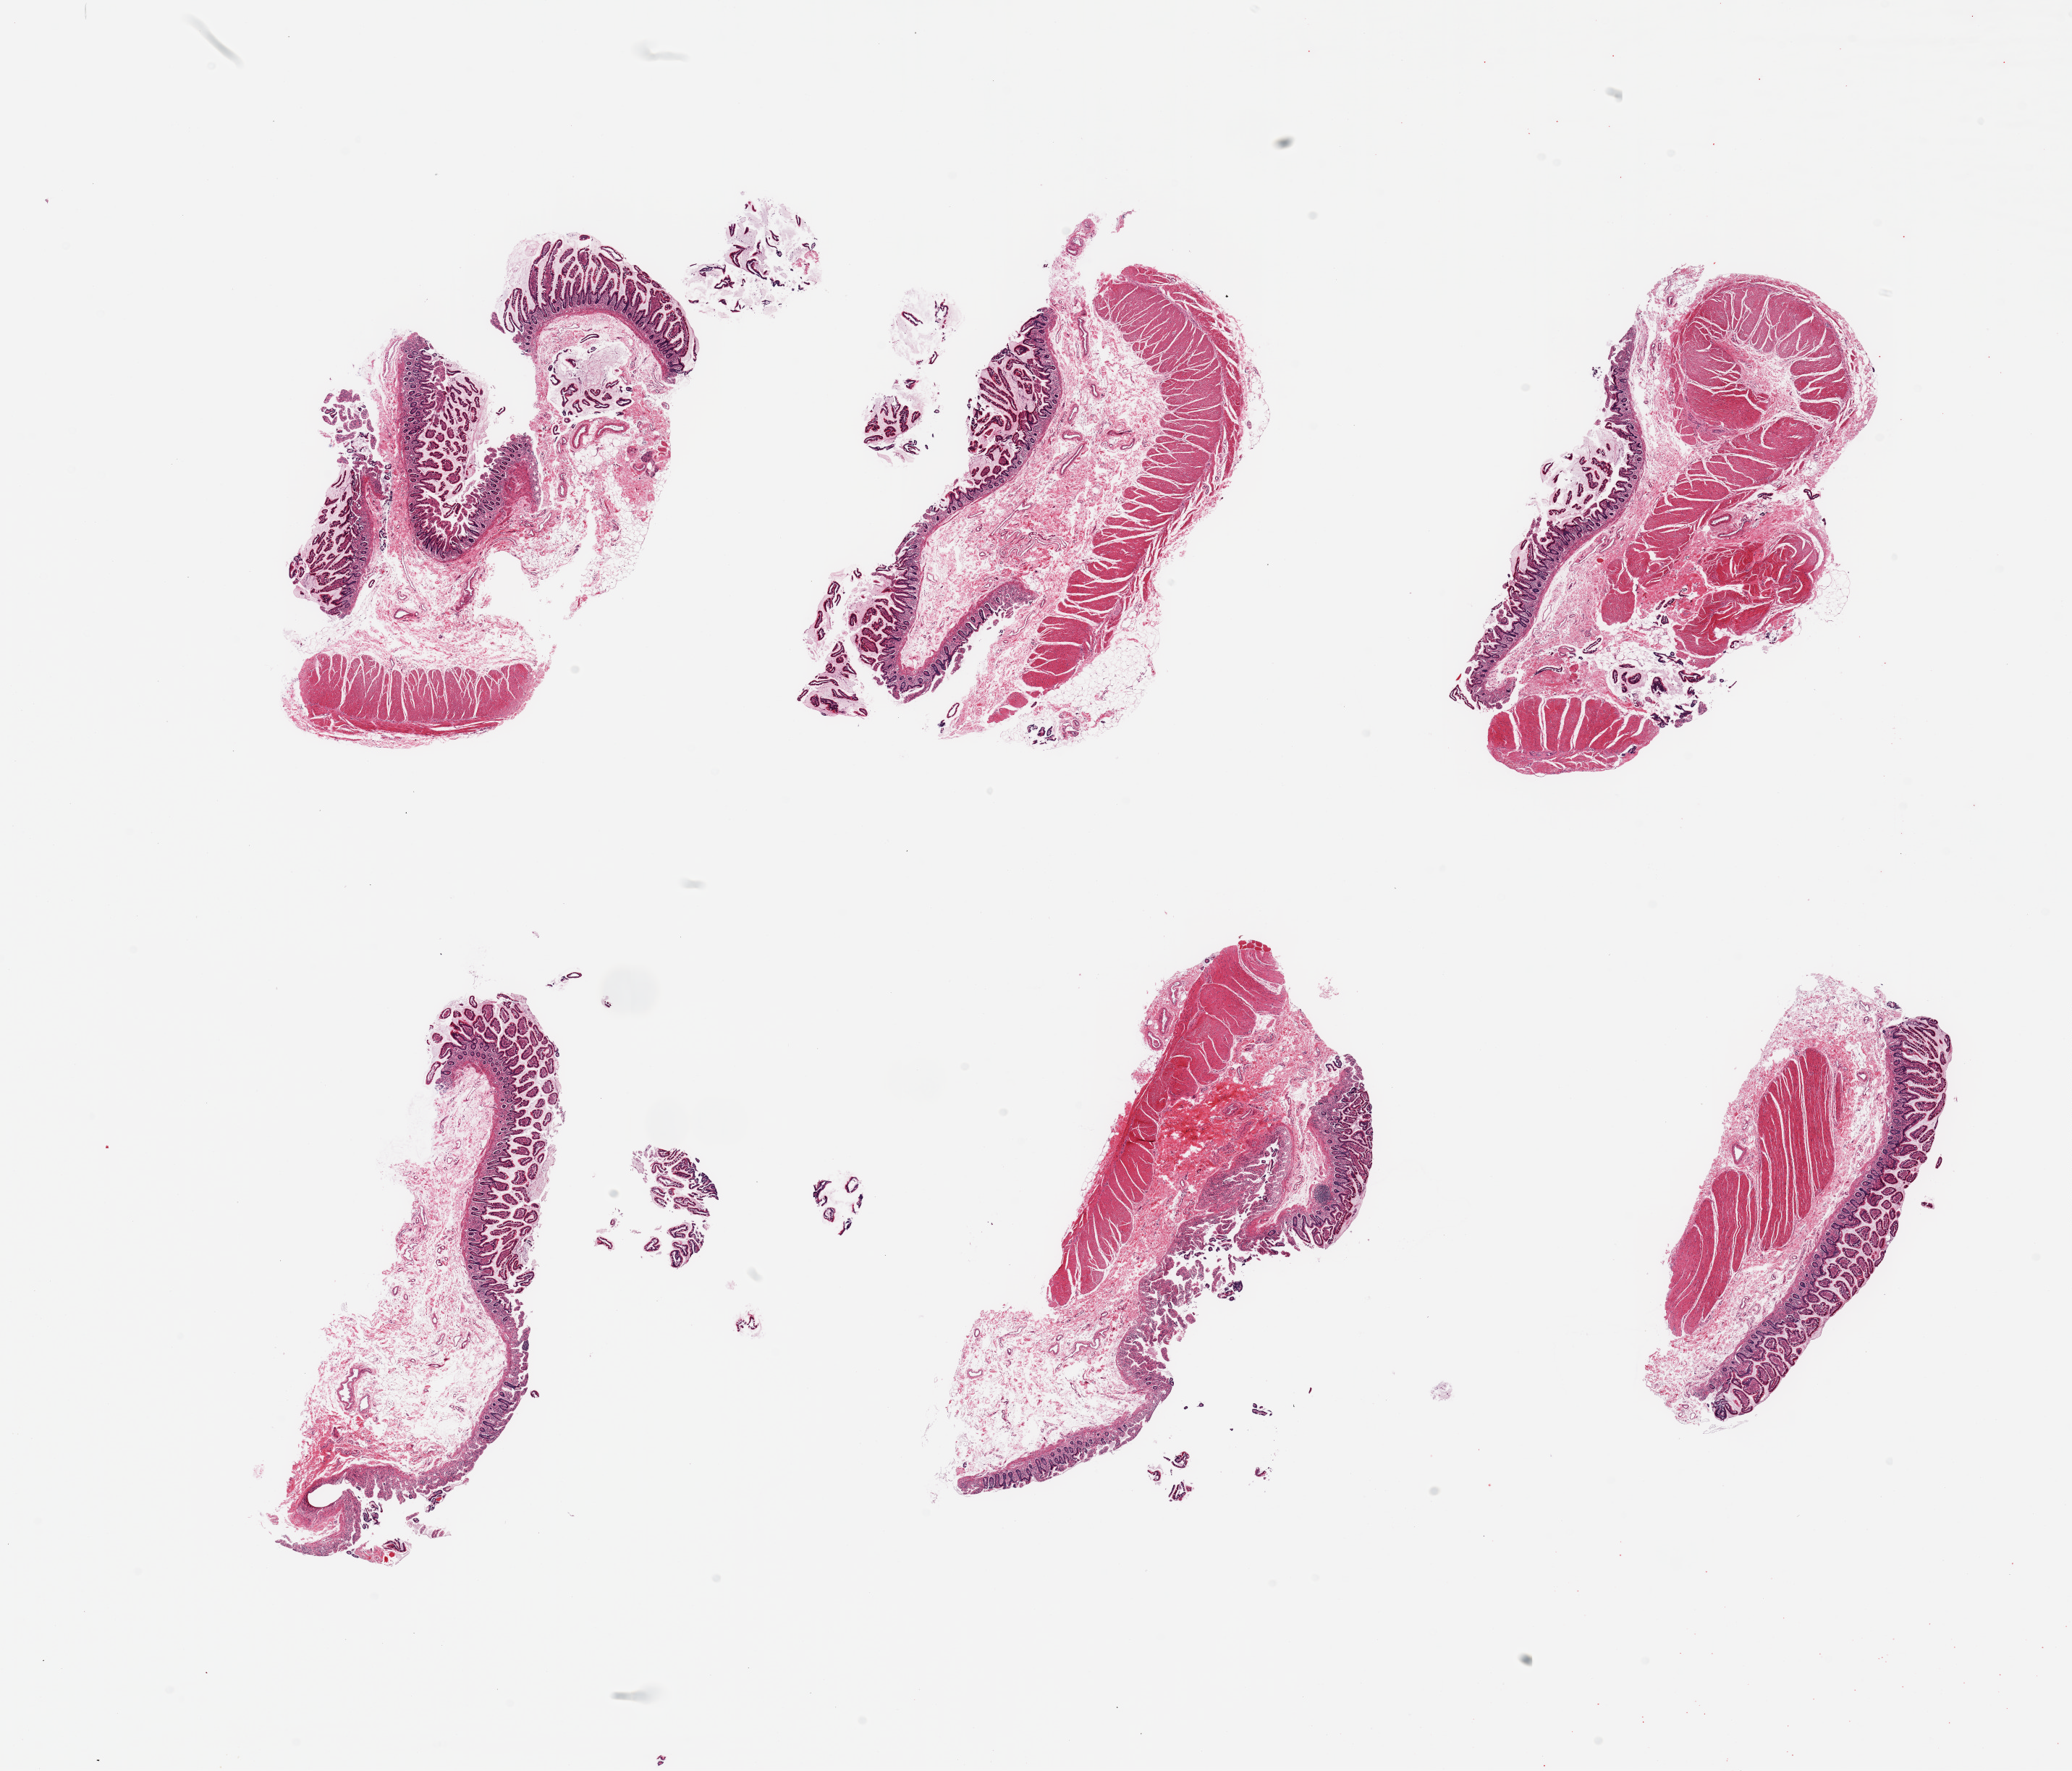
Whole-slide image, haematoxylin and eosin stain, a low-resolution overview of the entire scanned area, about 22.6 x 19.4 mm (from a 20x scan). PAXgene-fixed paraffin-embedded (PFPE) section. Section of ileum (target tissue). Donor tissue sample.
Reviewer comment on this tissue sample: 6 pieces; no lymphoid tissue; full thickness of wall.